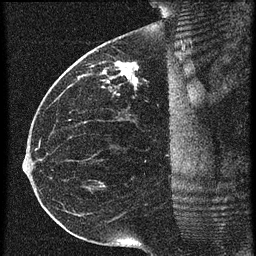
Breast MRI (dynamic contrast-enhanced), one sagittal slice; slice 30 of 60 in the series (ordered by position); 3 images stored at this slice position (order not interpretable as contrast timing); 1.5 T; TE 4.2 ms, TR 20.4 ms; 1.5 mm slice thickness; 256 × 256 image matrix, field of view 200 × 200 mm. Patient: female, 35 years. From the clinical record (not read from this slice): setting: breast cancer imaged before/during neoadjuvant chemotherapy; receptor status: HR-positive, HER2-negative.
Structures marked on this image (semi-automatically segmented with operator editing):
- analysis volume of interest (the breast-tissue region the enhancement analysis was run in; not a lesion): bounding box (x1, y1, x2, y2) in pixels: (84, 50, 179, 97)
- tumour enhancement mask (voxels above the 90 % enhancement threshold inside the analysis volume of interest): (104, 62, 139, 83)